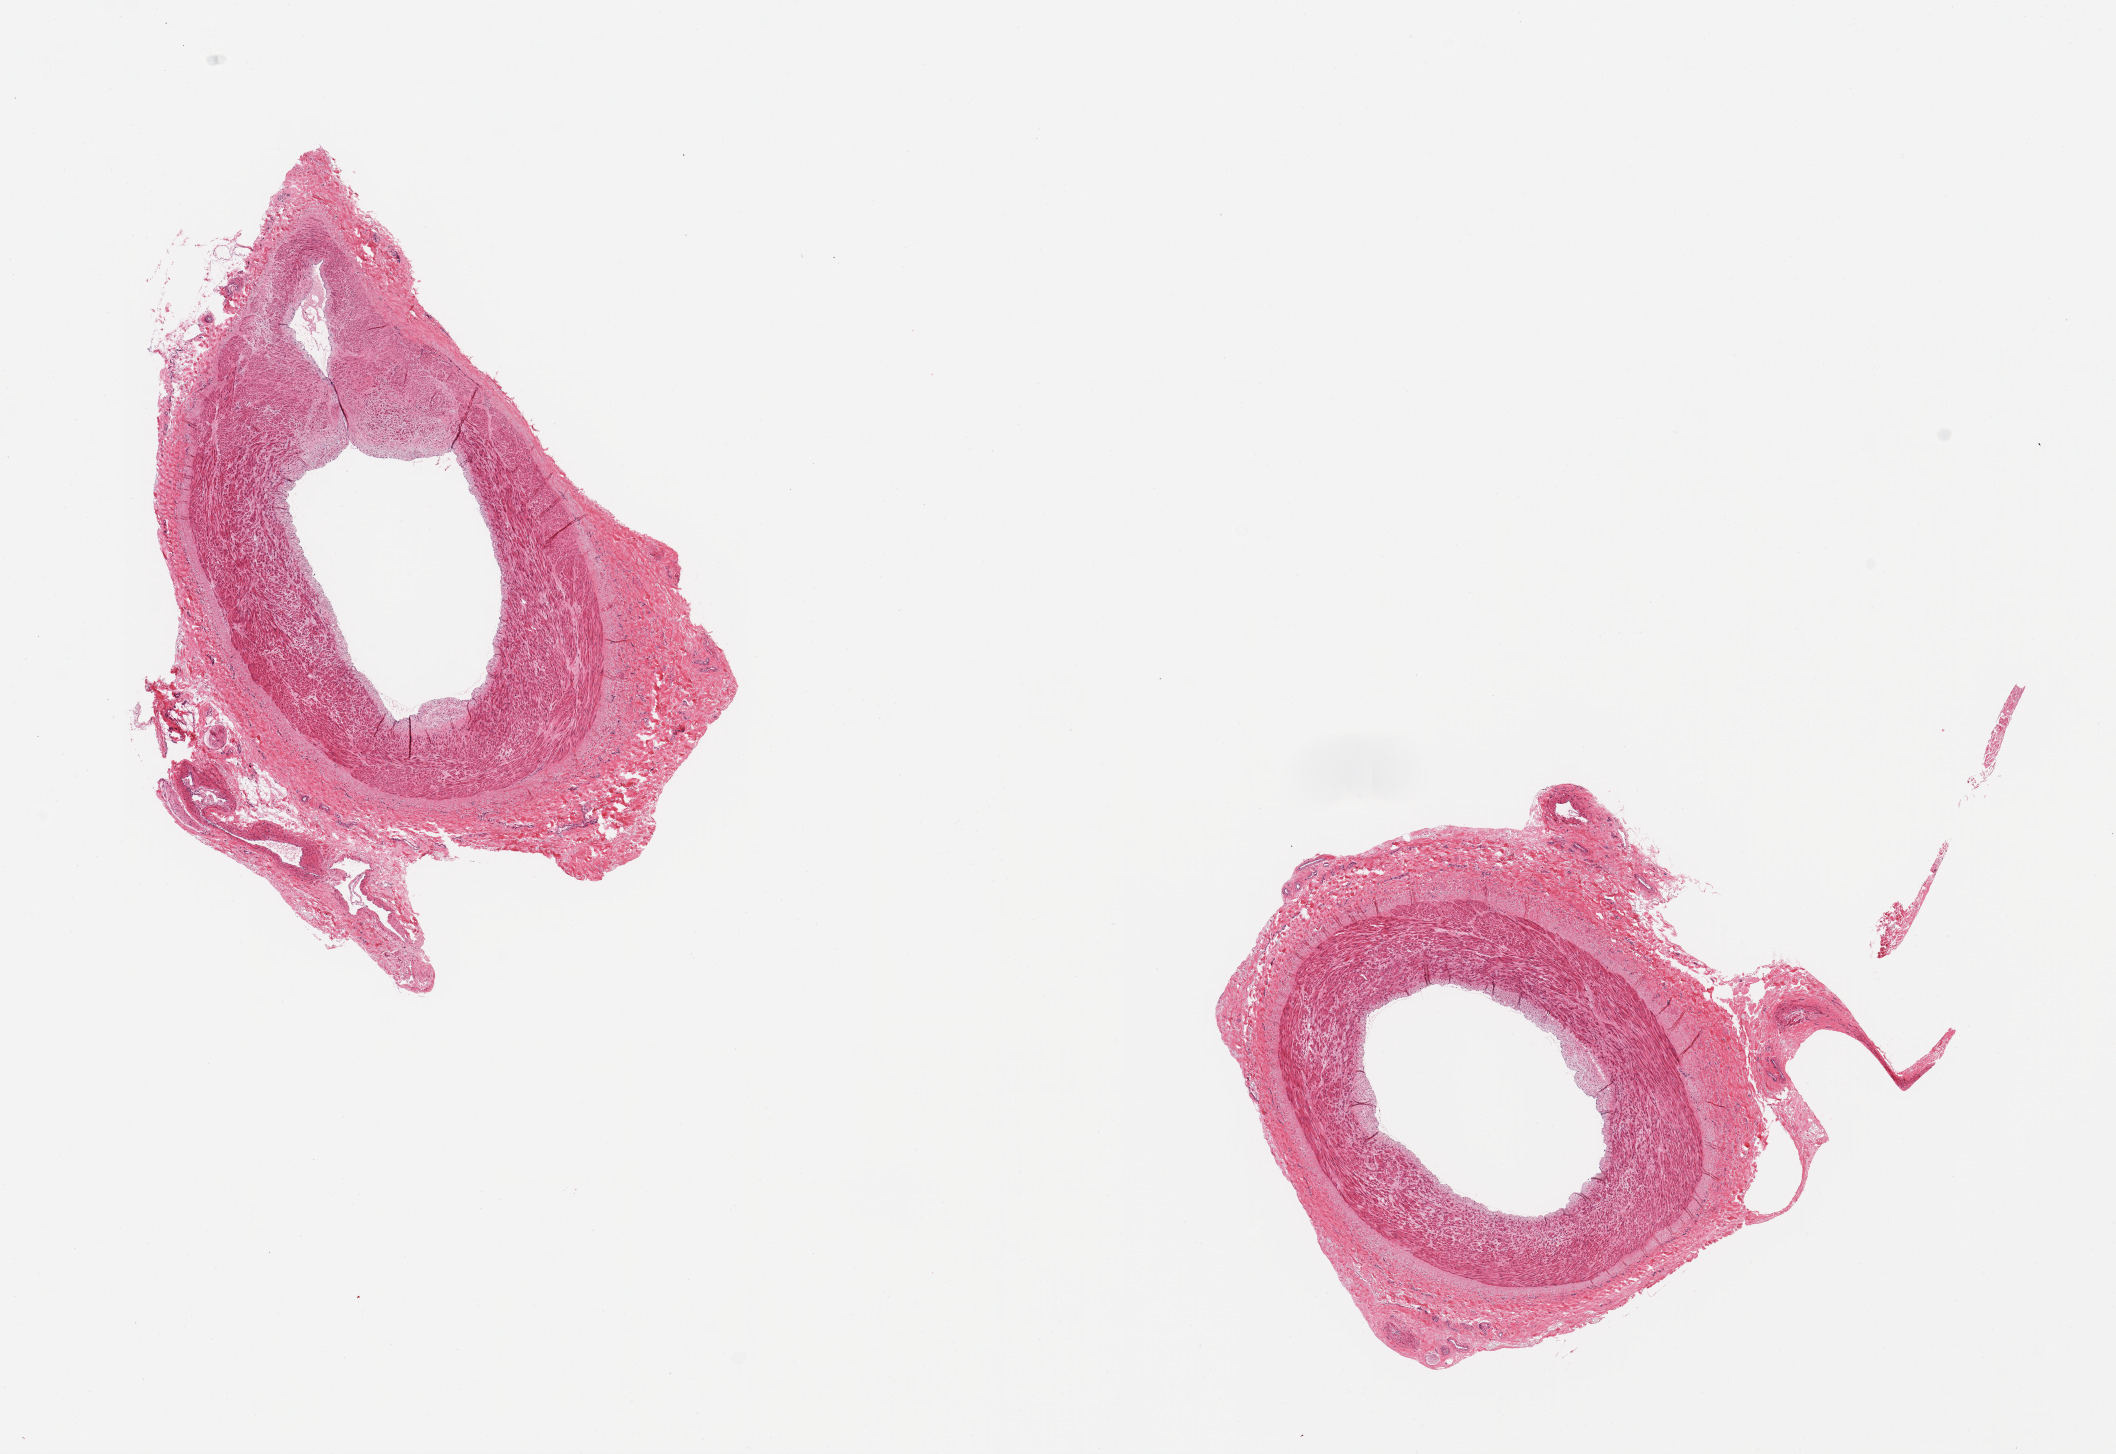
H&E whole-slide image, shown as a low-resolution overview of the whole scanned area (about 16.7 x 11.5 mm, from a 20x scan). PAXgene-fixed paraffin-embedded (PFPE) section. Sampled site (target tissue): tibial artery. Donor tissue sample. Donor: male.
Pathologist's review note for this sample: 2 pieces, rims/nubbin of adherent fibrous tissue, ~1mm.